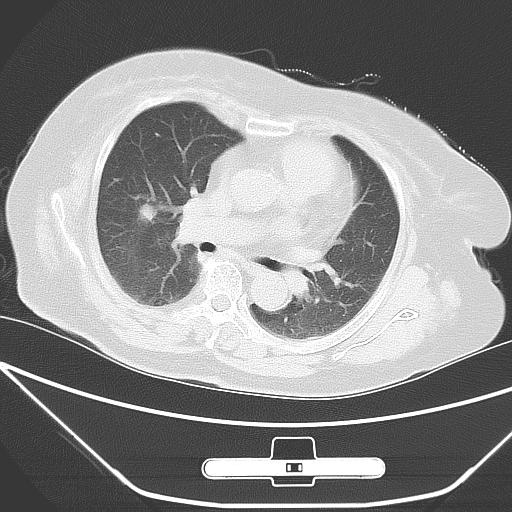
Chest CT, one axial slice. 120 kVp. Lung window (W 1500 / L -600 HU). 512 × 512 image matrix. Female patient, age 65 years. From the clinical record (not read from this slice): clinical TNM (as recorded): T1c N0 M0.
Annotated regions visible in this slice (rectangle marked by the reading radiologist):
- lung tumour (recorded histology: adenocarcinoma): bounding box [x1, y1, x2, y2] px = [128, 192, 163, 238]